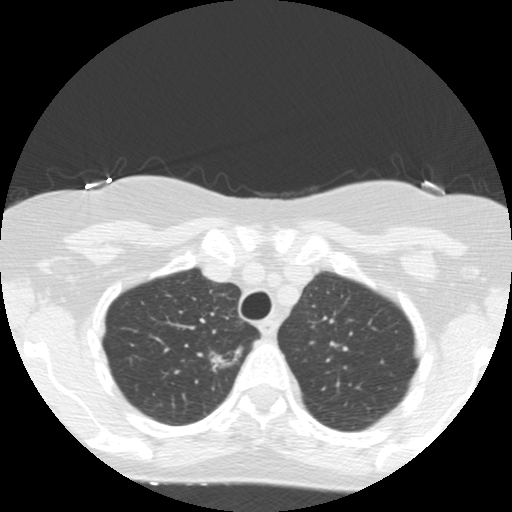
Low-dose screening chest CT, one axial slice; position 123 of 155 along the scan axis; 120 kVp; lung window (W 1500 / L -600 HU); 2.5 mm slice thickness; 512 × 512 image matrix, field of view 300 × 300 mm.
Structures marked on this image (outlined manually by an expert reader):
- lesion 1 (tumor, upper lobe of right lung): bounding box [x1, y1, x2, y2] px = [210, 346, 243, 372]